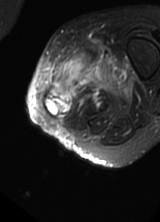
MRI of an extremity soft-tissue mass, one axial slice. Position 14 of 69 along the scan axis. T2-weighted fat-saturated. MR volume resampled by the dataset authors to the PET/CT grid (not the native acquisition matrix). 3.27 mm slice thickness. 160 × 222 image matrix. Female patient. Case-level facts recorded for this patient, not image findings: histological type: pleomorphic leiomyosarcoma; grade: high; site of the primary tumour: left thigh.
Annotated regions visible in this slice (expert contour drawn on MRI and transferred to this co-registered scan by the dataset authors):
- gross tumour volume including surrounding oedema: bounding box (x1, y1, x2, y2) in pixels: (43, 50, 131, 119)
- gross tumour volume (mass): (45, 95, 71, 117)